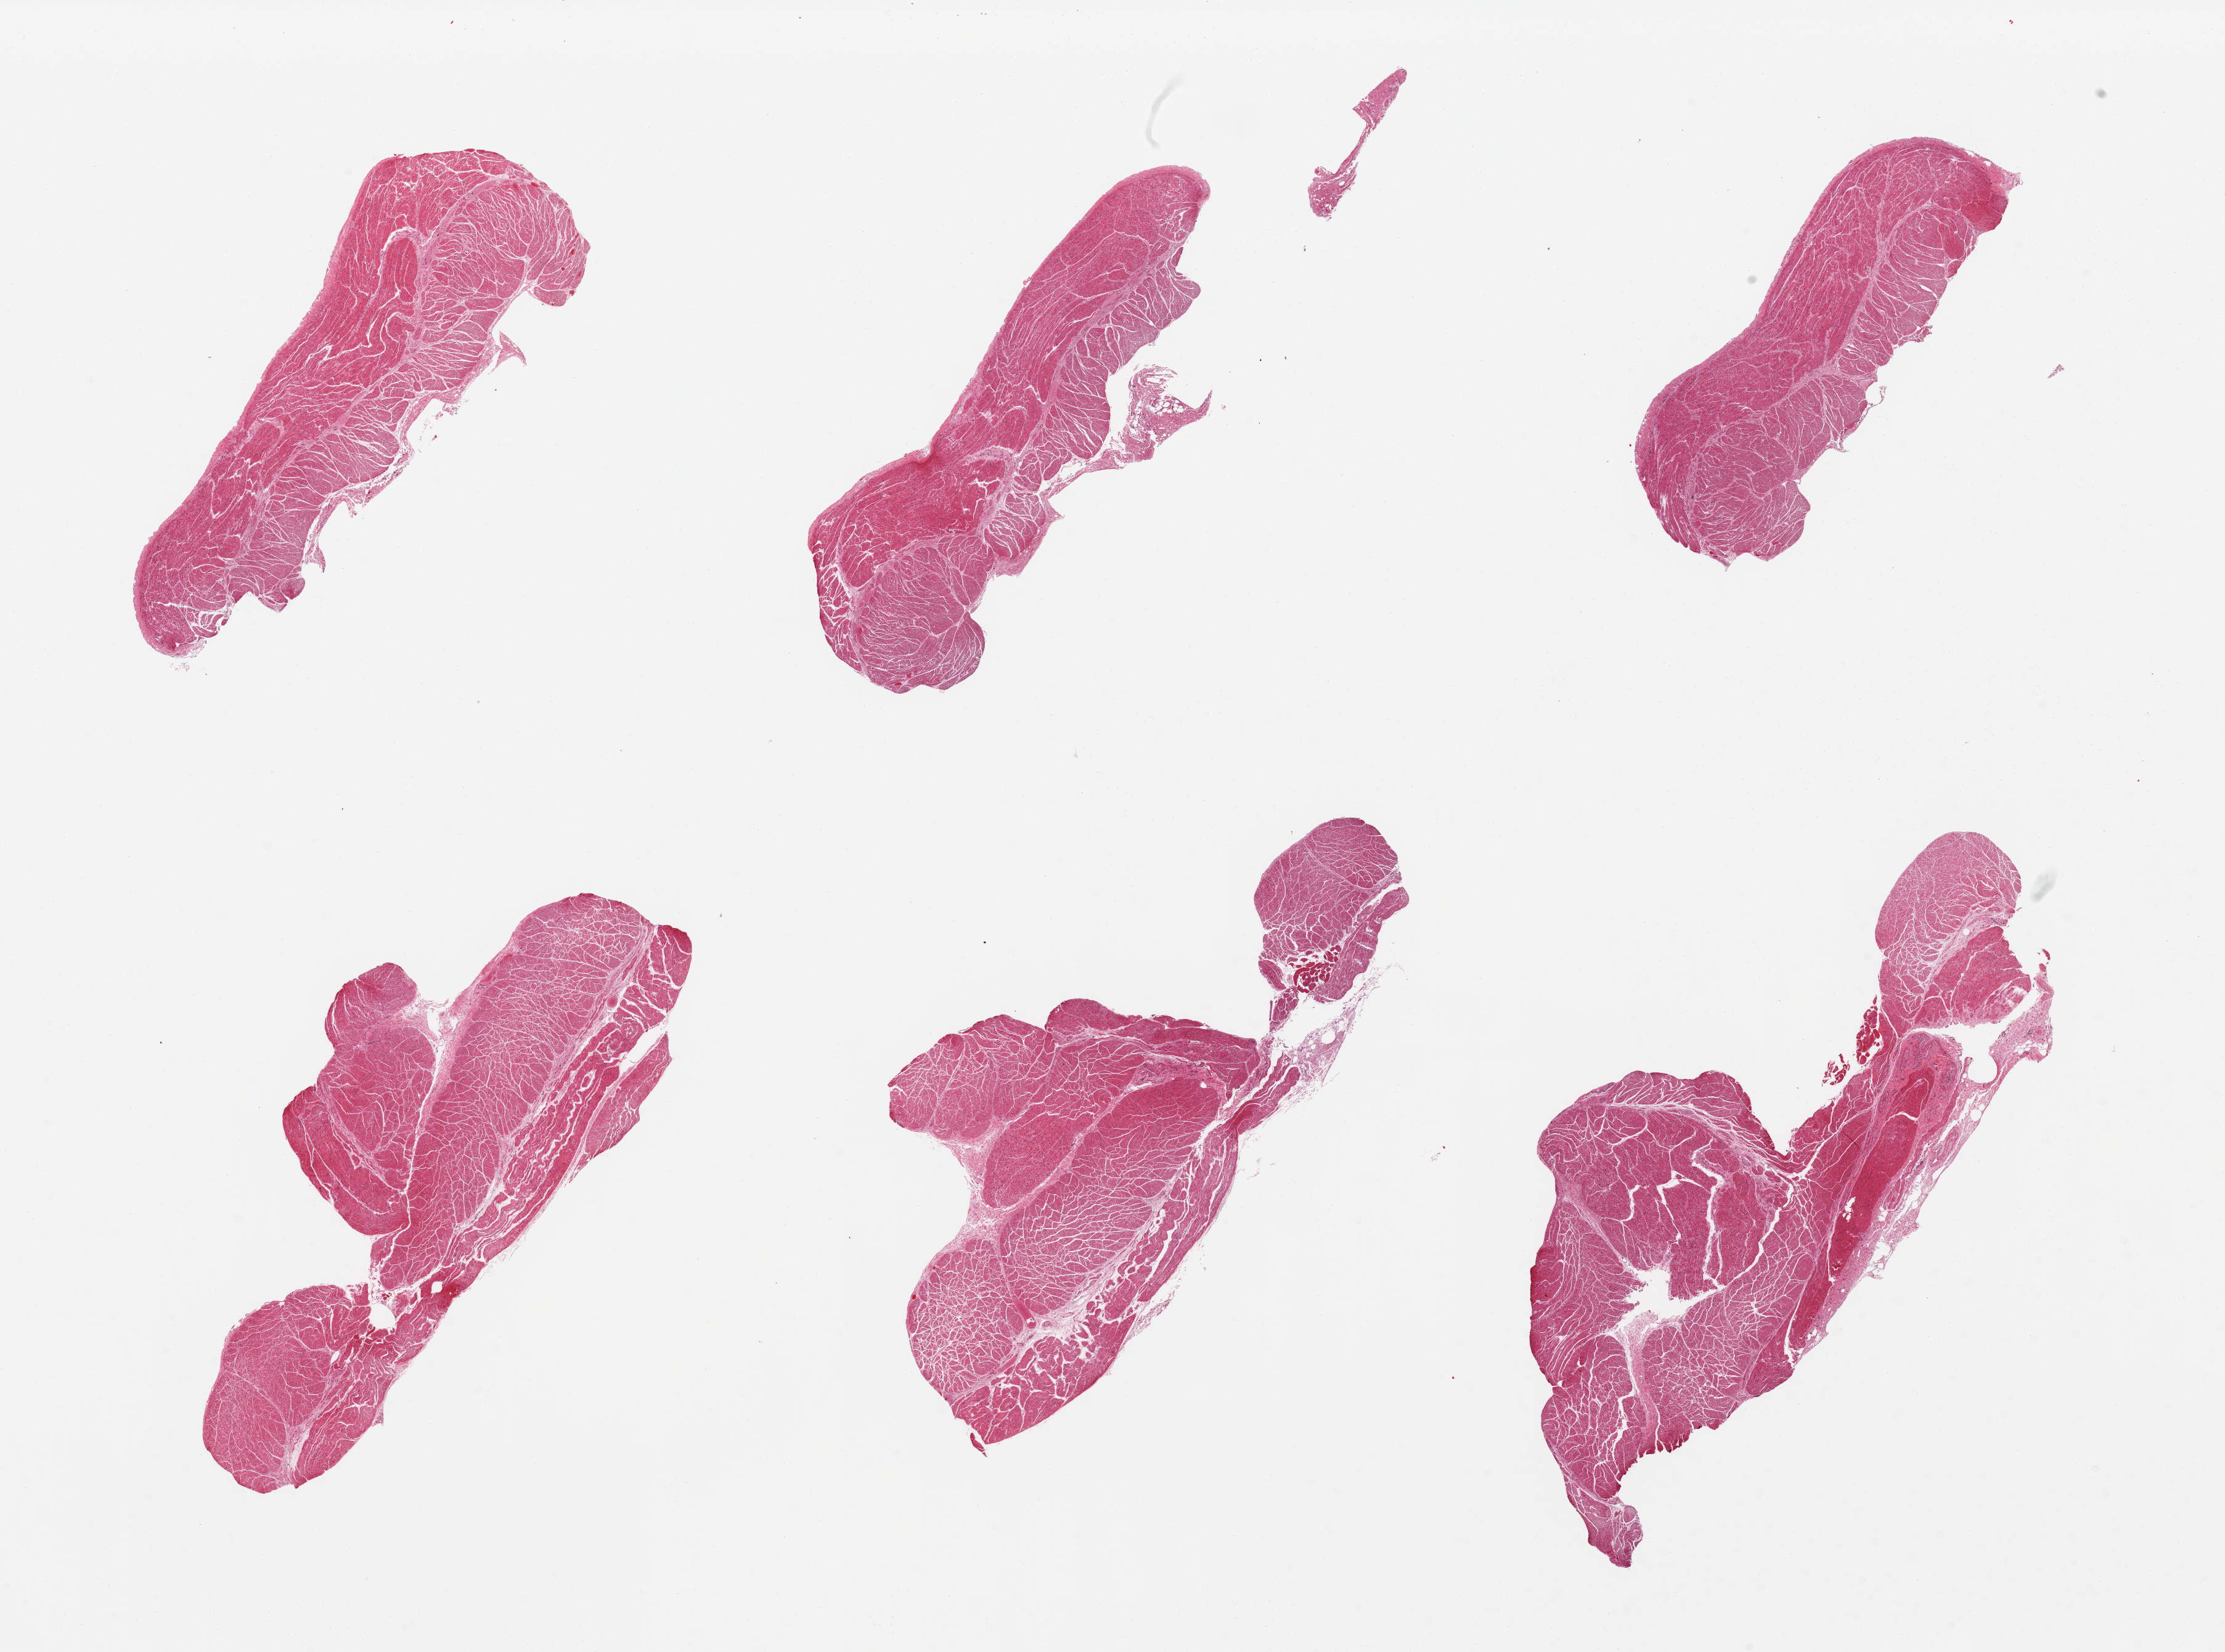
Hematoxylin and eosin (H&E) whole-slide image — whole scanned area (about 28.5 x 21.2 mm, acquisition: 20x scan) shown as a low-resolution overview, PAXgene-fixed paraffin-embedded (PFPE) section, target tissue: esophageal muscle, donor tissue sample. Donor: female.
Pathologist's review note for this sample: 6 pieces, all muscularis.